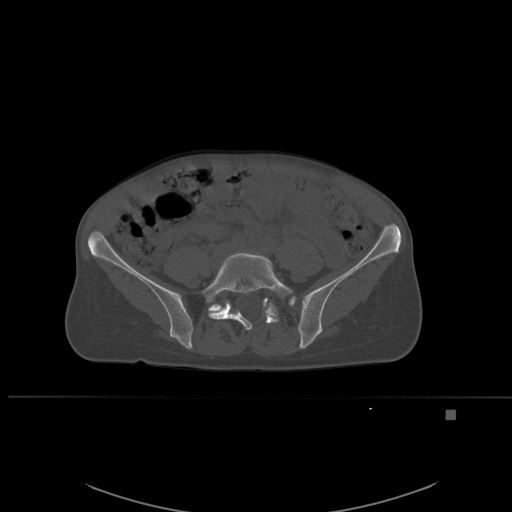
CT including the spine, one axial slice; slice 171 of 537 in the series (ordered by position); bone window (W 1800 / L 400 HU); 512 × 512 image matrix. Patient: female, 45 years. From the clinical record (not read from this slice): primary cancer: lung.
Annotated regions visible in this slice (semi-automatic segmentation, software-assisted and operator-edited):
- L5 vertebra: bounding box <201,251,297,330> (left, top, right, bottom; pixels)